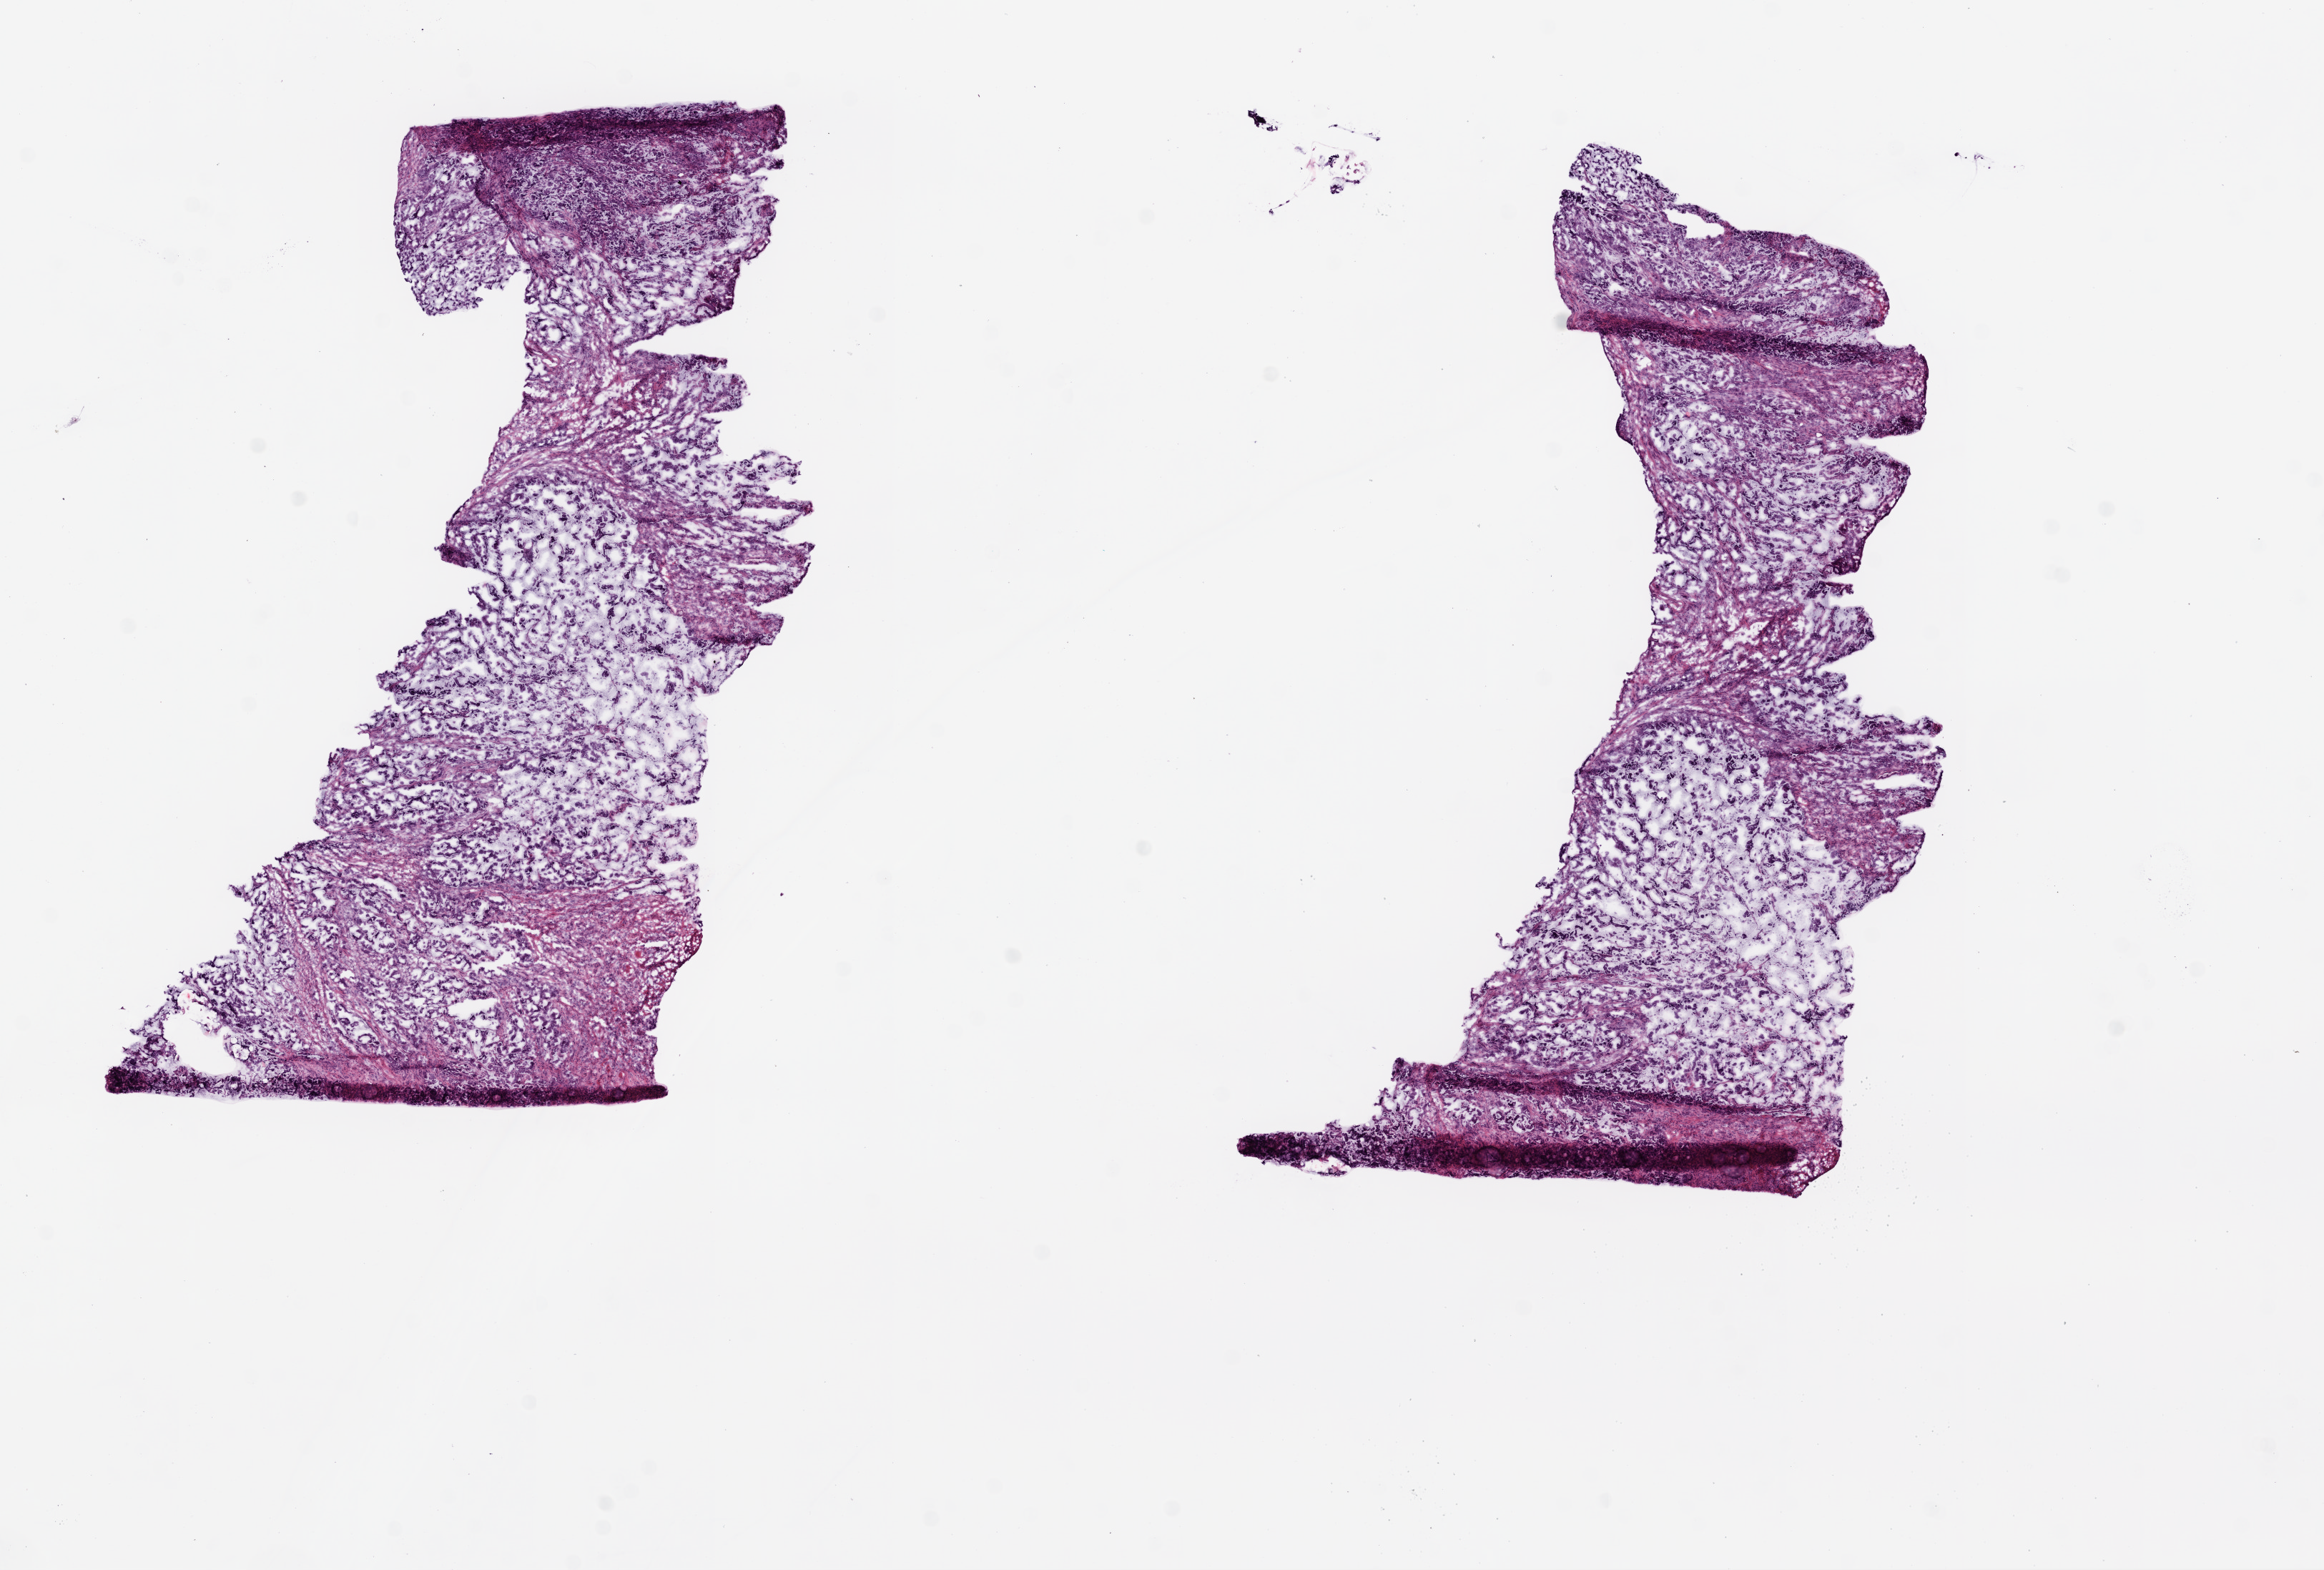
H&E whole-slide image, low-resolution overview of the scanned area, about 13.0 x 8.8 mm. Frozen section. Primary tumour sample from the stomach. Patient: male, age at initial diagnosis 76 years. Histologic grade: G3 (poorly differentiated). Pathologist review of this section (percent, as recorded): tumour cells 55%, tumour nuclei 70%, normal cells 0%, stromal cells 40%, necrosis 5%.
* lymph nodes positive (case pathology): 2 of 20 examined
* AJCC pathologic stage: IIB
* pathologic diagnosis: Adenocarcinoma with mixed subtypes